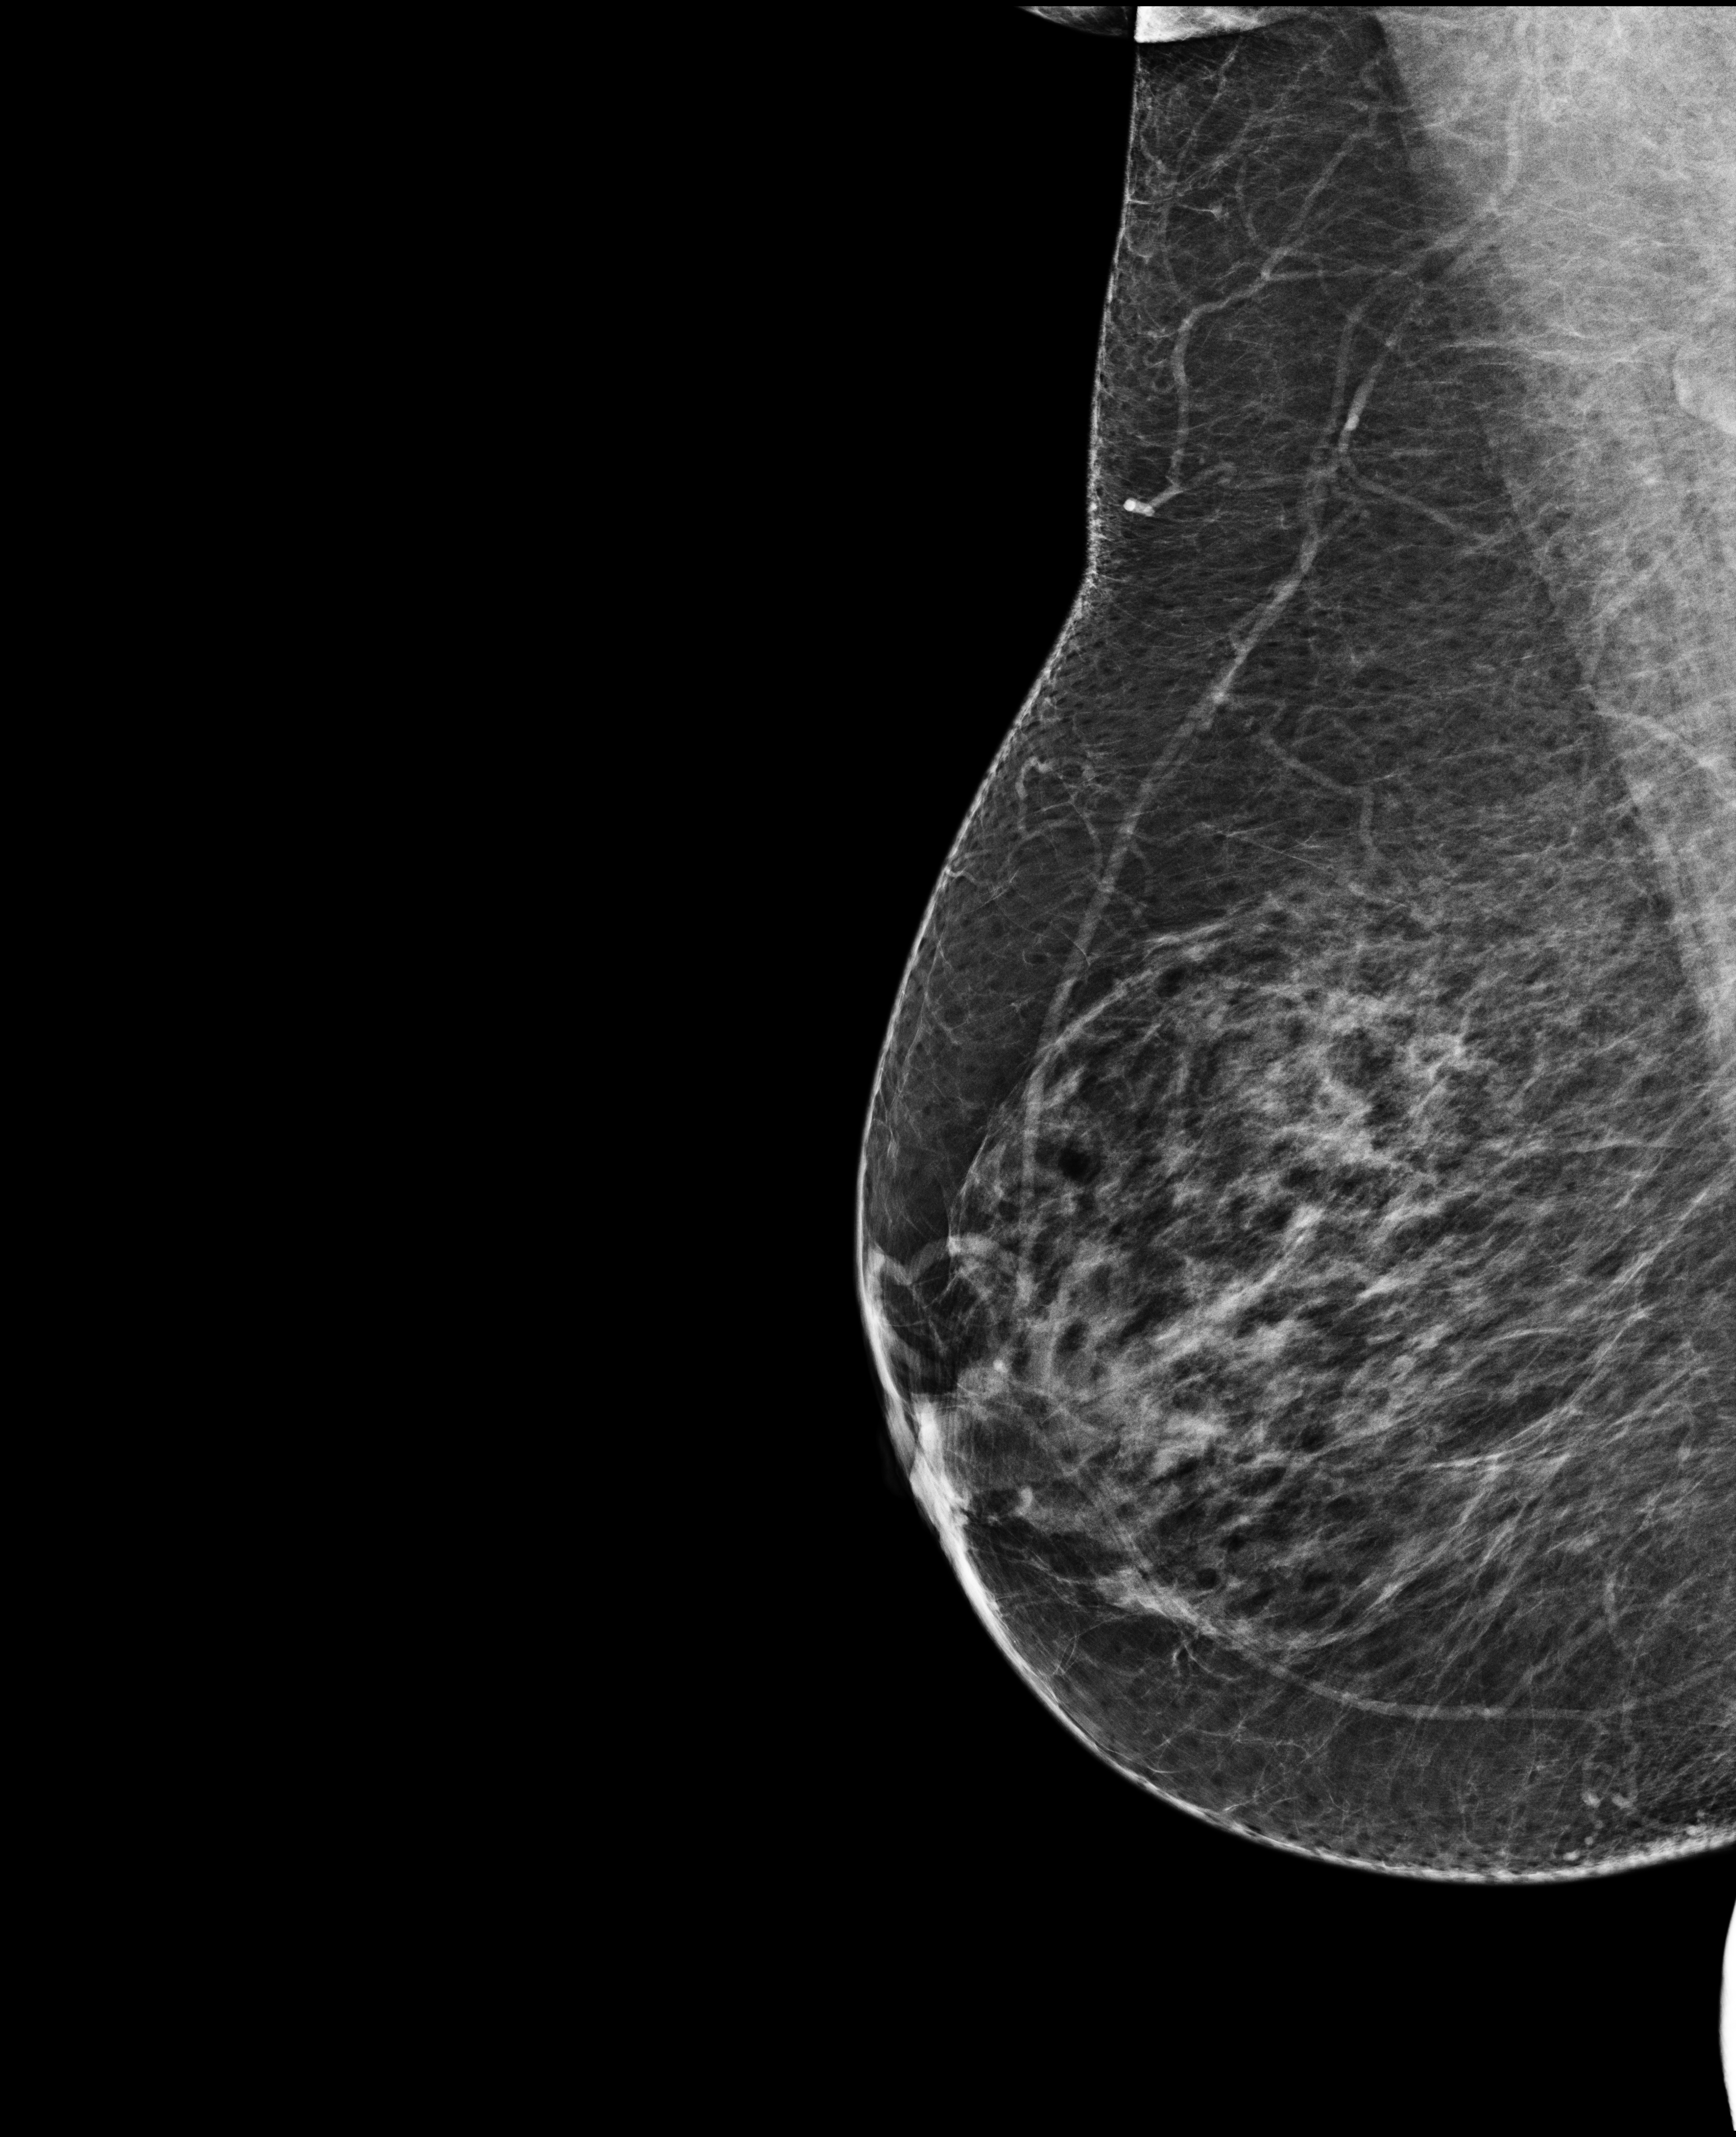
Annual screening mammography examination, compressed breast thickness 53 mm. Patient aged 72 years (female).
Image type: full-field digital mammogram. Breast: right. Projection: MLO view.